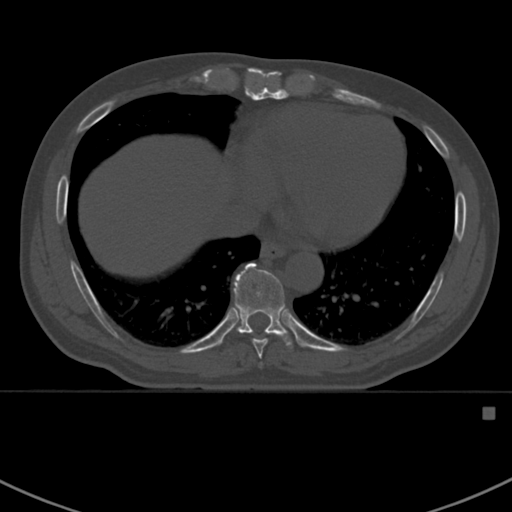
CT including the spine, one axial slice. Reconstruction kernel Br40s. 120 kVp. Bone window (W 1800 / L 400 HU). 1.5 mm slice thickness. 512 × 512 image matrix, field of view 358 × 358 mm. Patient: male, 59 years. From the clinical record (not read from this slice): primary cancer: prostate.
Structures marked on this image (semi-automatically segmented with operator editing):
- T8 vertebra: bounding box [x1, y1, x2, y2] px = [252, 334, 276, 359]
- T9 vertebra: [221, 262, 302, 350]